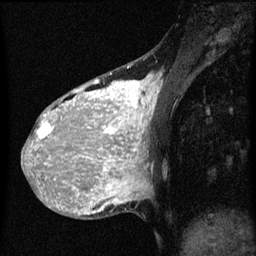
Breast MRI (dynamic contrast-enhanced), one sagittal slice; position 18 of 60 along the scan axis; dynamic contrast-enhanced series, image 2 of 3 at this slice position (ordered by acquisition); 1.5 T; TE 4.2 ms, TR 8 ms; 2 mm slice thickness; 256 × 256 image matrix. Female patient, age 36 years.
Annotated regions visible in this slice (semi-automatically segmented with operator editing):
- analysis volume of interest (the breast-tissue region the enhancement analysis was run in; not a lesion): bounding box [x1, y1, x2, y2] px = [32, 68, 163, 161]
- tumour enhancement mask (voxels above the 70 % enhancement threshold inside the analysis volume of interest): [32, 76, 159, 161]